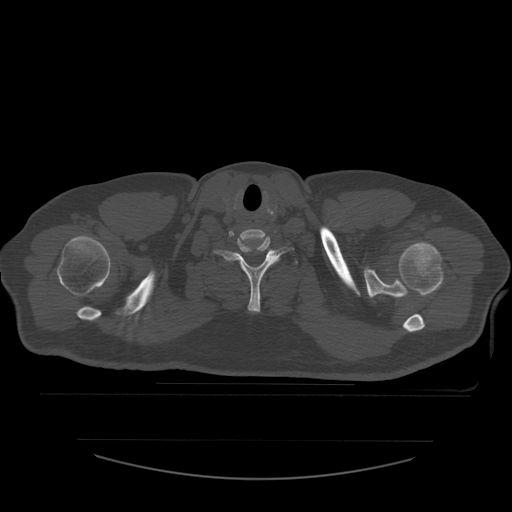
CT including the spine, one axial slice. Position 483 of 532 along the scan axis. 120 kVp. Bone window (W 1800 / L 400 HU). 1.25 mm slice thickness. 512 × 512 image matrix, field of view 441 × 441 mm. Patient age 44 years. From the clinical record (not read from this slice): primary cancer: soft tissue sarcoma.
Outlined on this slice (semi-automatically segmented with operator editing):
- T1 vertebra: bounding box <296,261,298,264> (left, top, right, bottom; pixels)